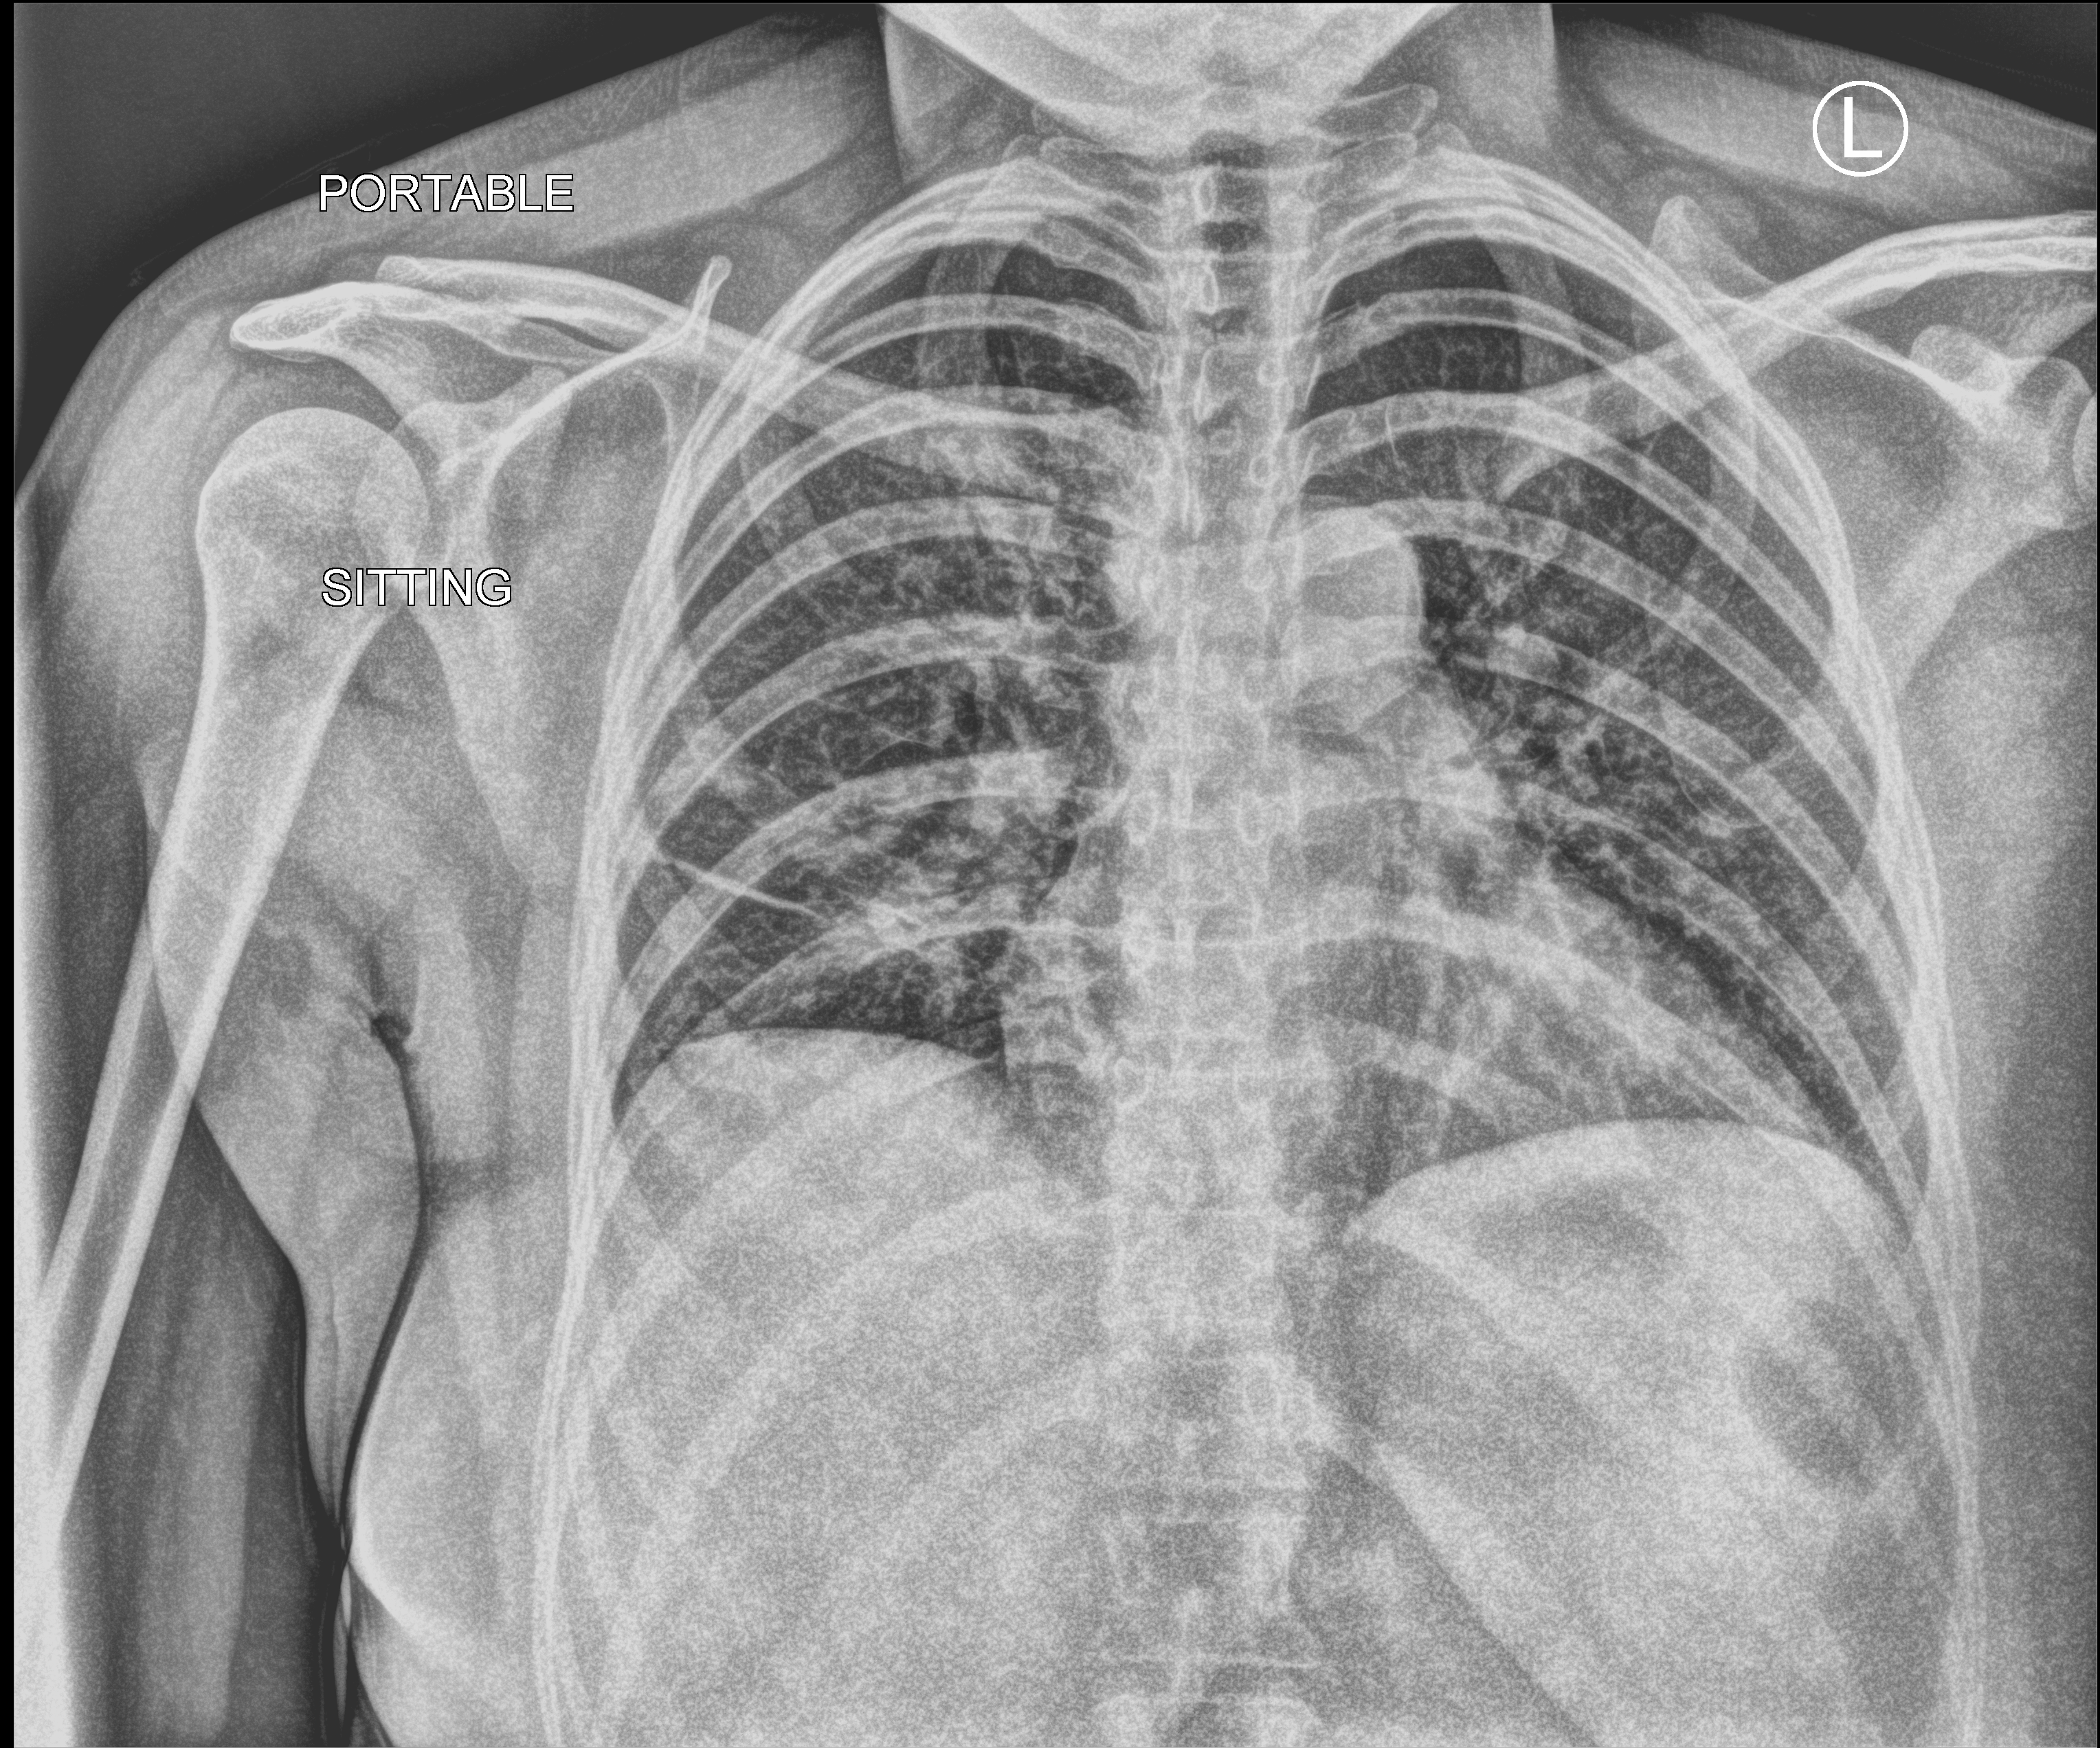
Portable chest radiograph; anteroposterior (AP) projection. Female patient hospitalised with COVID-19, age 18–59 years.
Hospital-stay facts (about this admission, not read from this image; timing relative to this image not recorded):
- admitted to intensive care during this hospital stay: no
- mechanically ventilated during this hospital stay: no
- other chronic lung disease (admission record): no